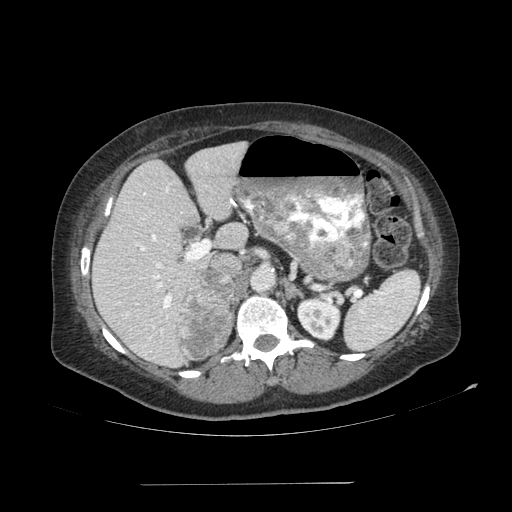
Contrast-enhanced abdominal CT, one axial slice; slice 65 of 113 in the series (ordered by position); reconstruction kernel SOFT; 120 kVp; soft-tissue window (W 400 / L 40 HU); 2.5 mm slice thickness; 512 × 512 image matrix, field of view 440 × 440 mm. Patient: female, 67 years. From the clinical record (not read from this slice): diagnosis: adrenocortical carcinoma; tumour side: right adrenal; tumour size at pathology: 9.8 cm; Ki-67 index: 59 %; stage (as recorded): 4.
Outlined on this slice (semi-automatic segmentation, software-assisted and operator-edited):
- mass: box from (x=176, y=273) to (x=235, y=358) px